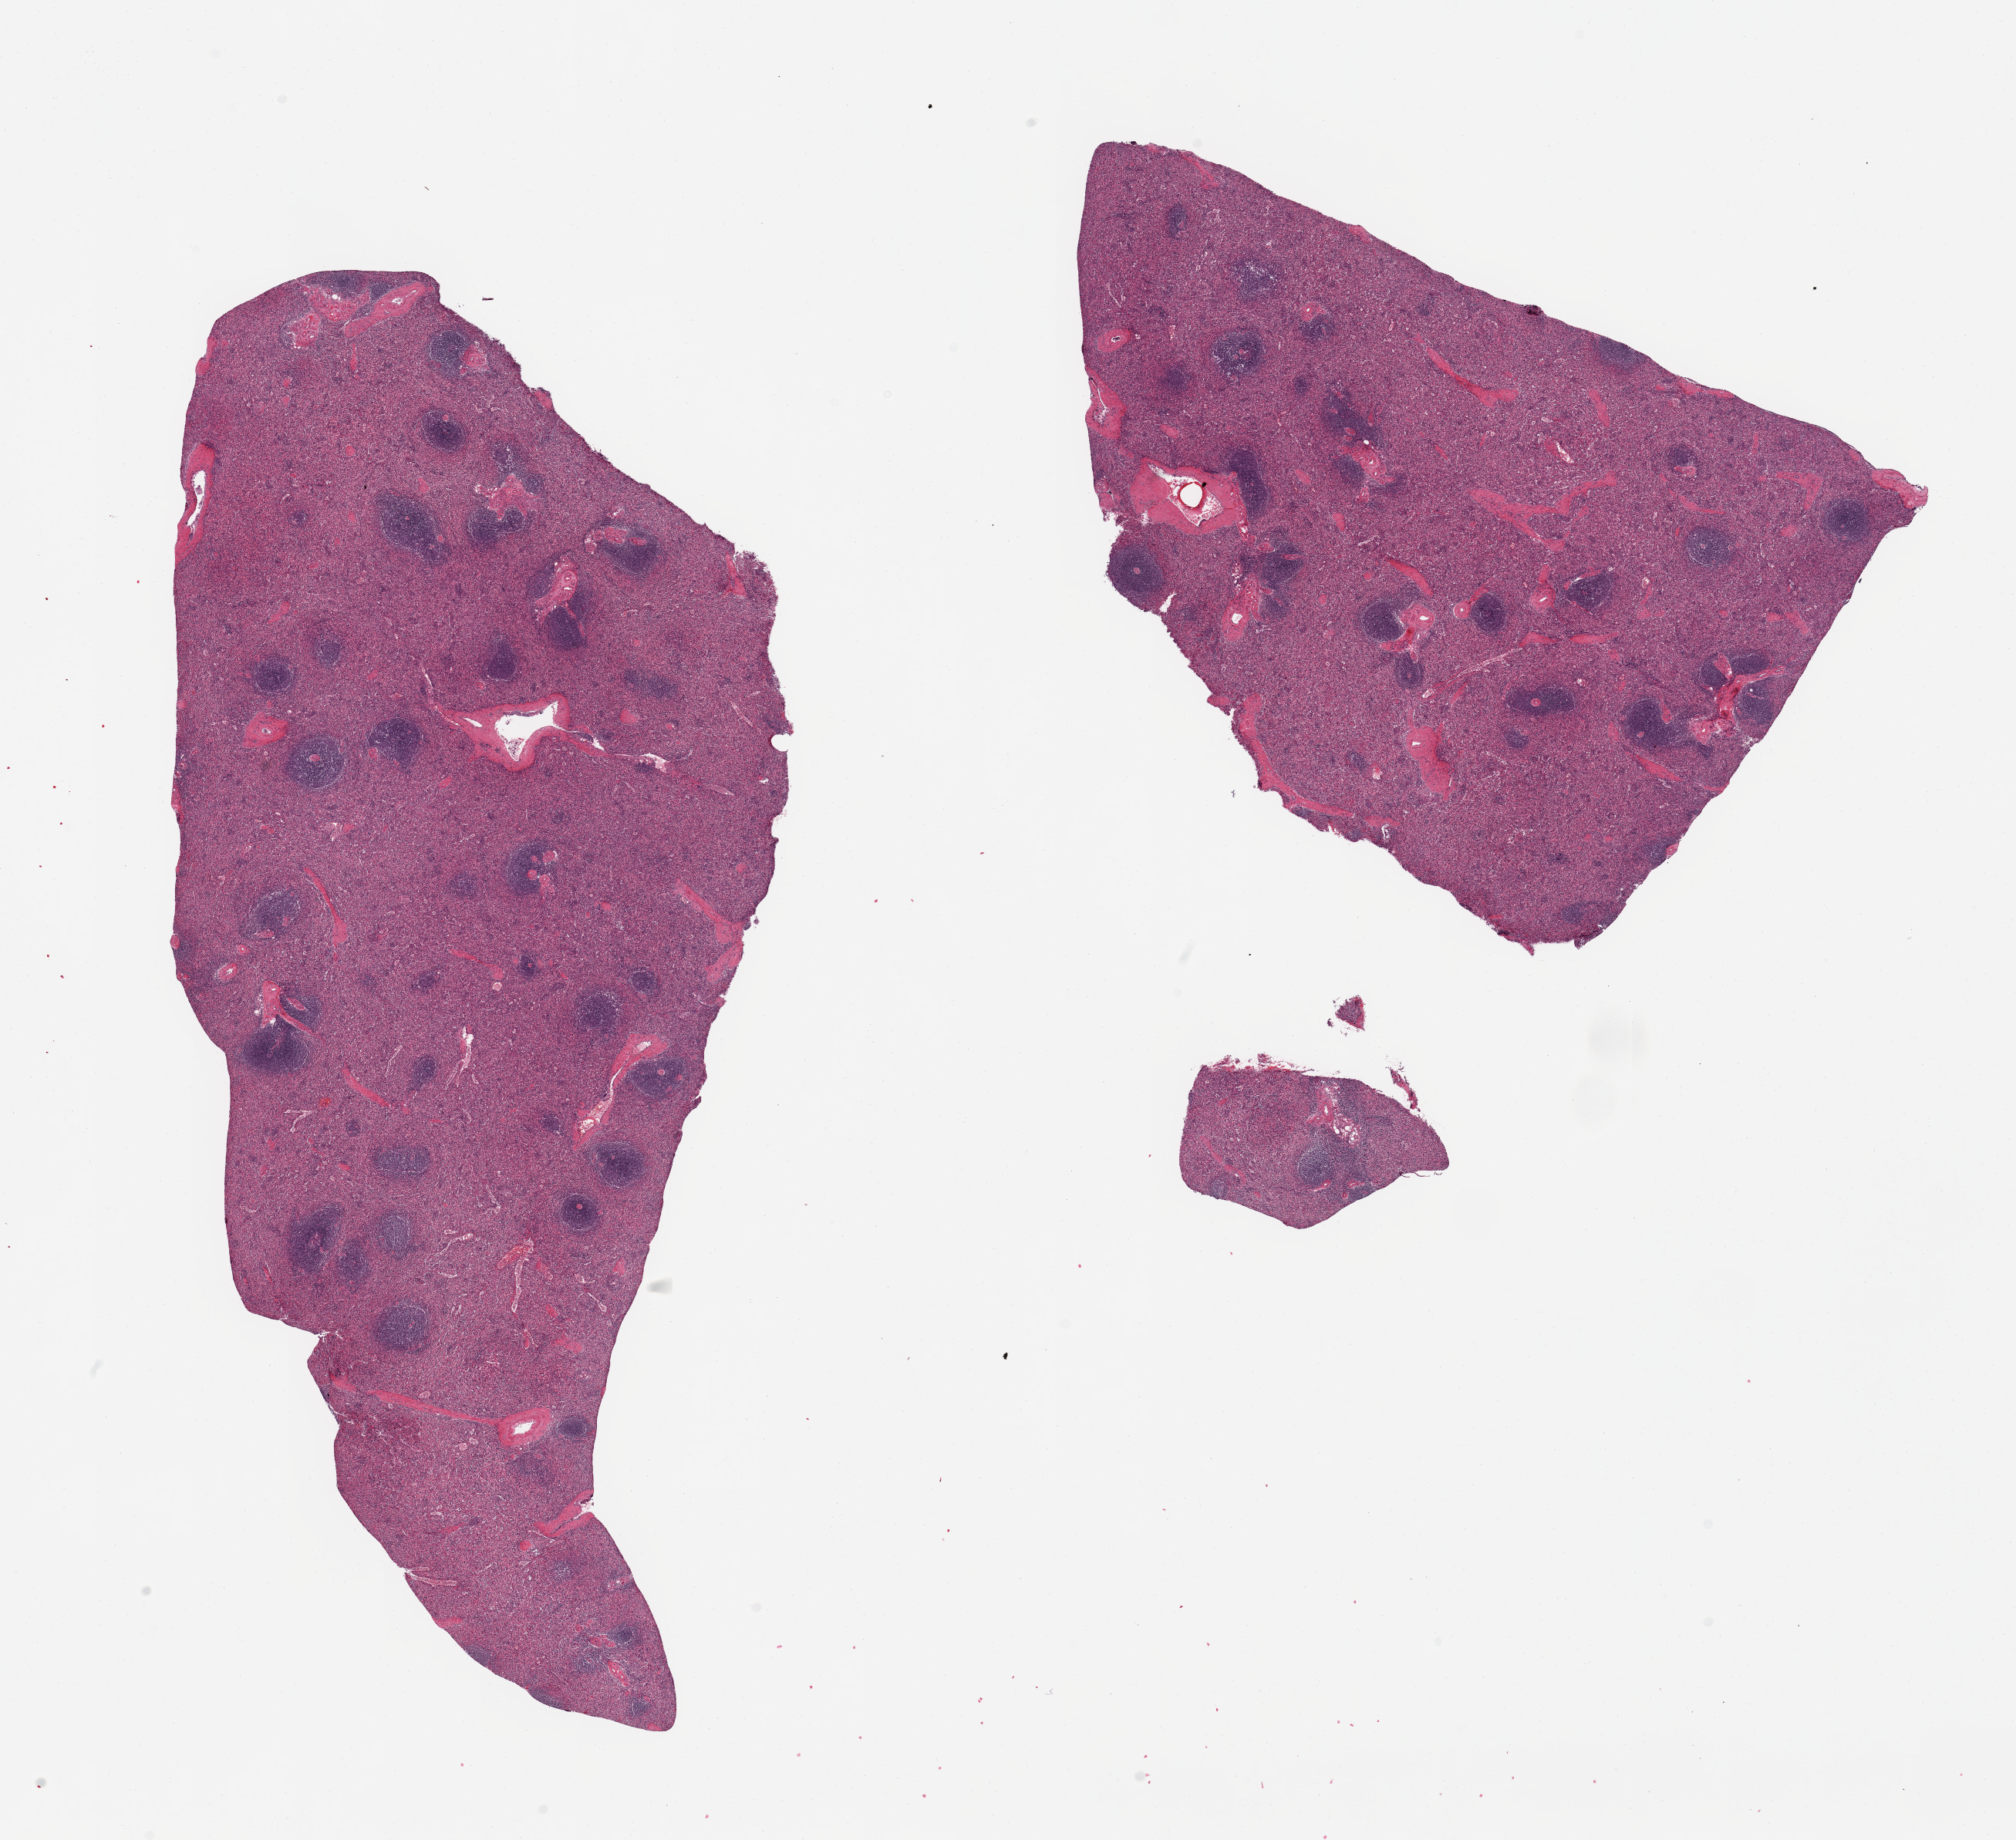
H&E whole-slide image, brightfield — whole scanned area (about 20.7 x 18.9 mm) shown as a low-resolution overview, PAXgene-fixed paraffin-embedded (PFPE) section, section of spleen (target tissue), donor tissue sample. Donor sex: female.
Pathologist's review note for this sample: 2 pieces; no congestion.